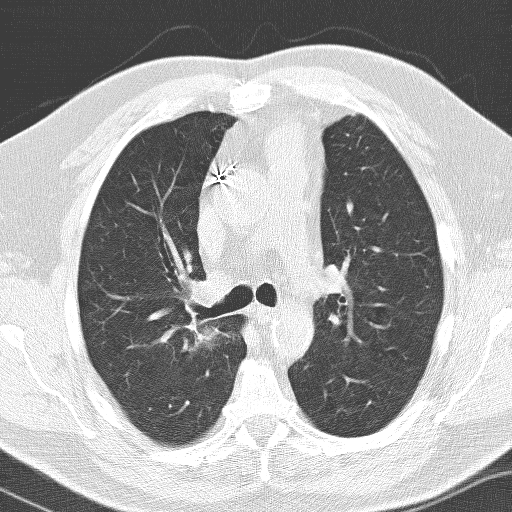
Low-dose screening chest CT, one axial slice. Slice 99 of 141 in the series (ordered by position). 120 kVp. Lung window (W 1500 / L -600 HU). 3.2 mm slice thickness. 512 × 512 image matrix, field of view 326 × 326 mm.
Structures marked on this image (expert manual segmentation):
- lesion 1 (tumor, upper lobe of right lung): bounding box (x1, y1, x2, y2) in pixels: (195, 327, 226, 347)